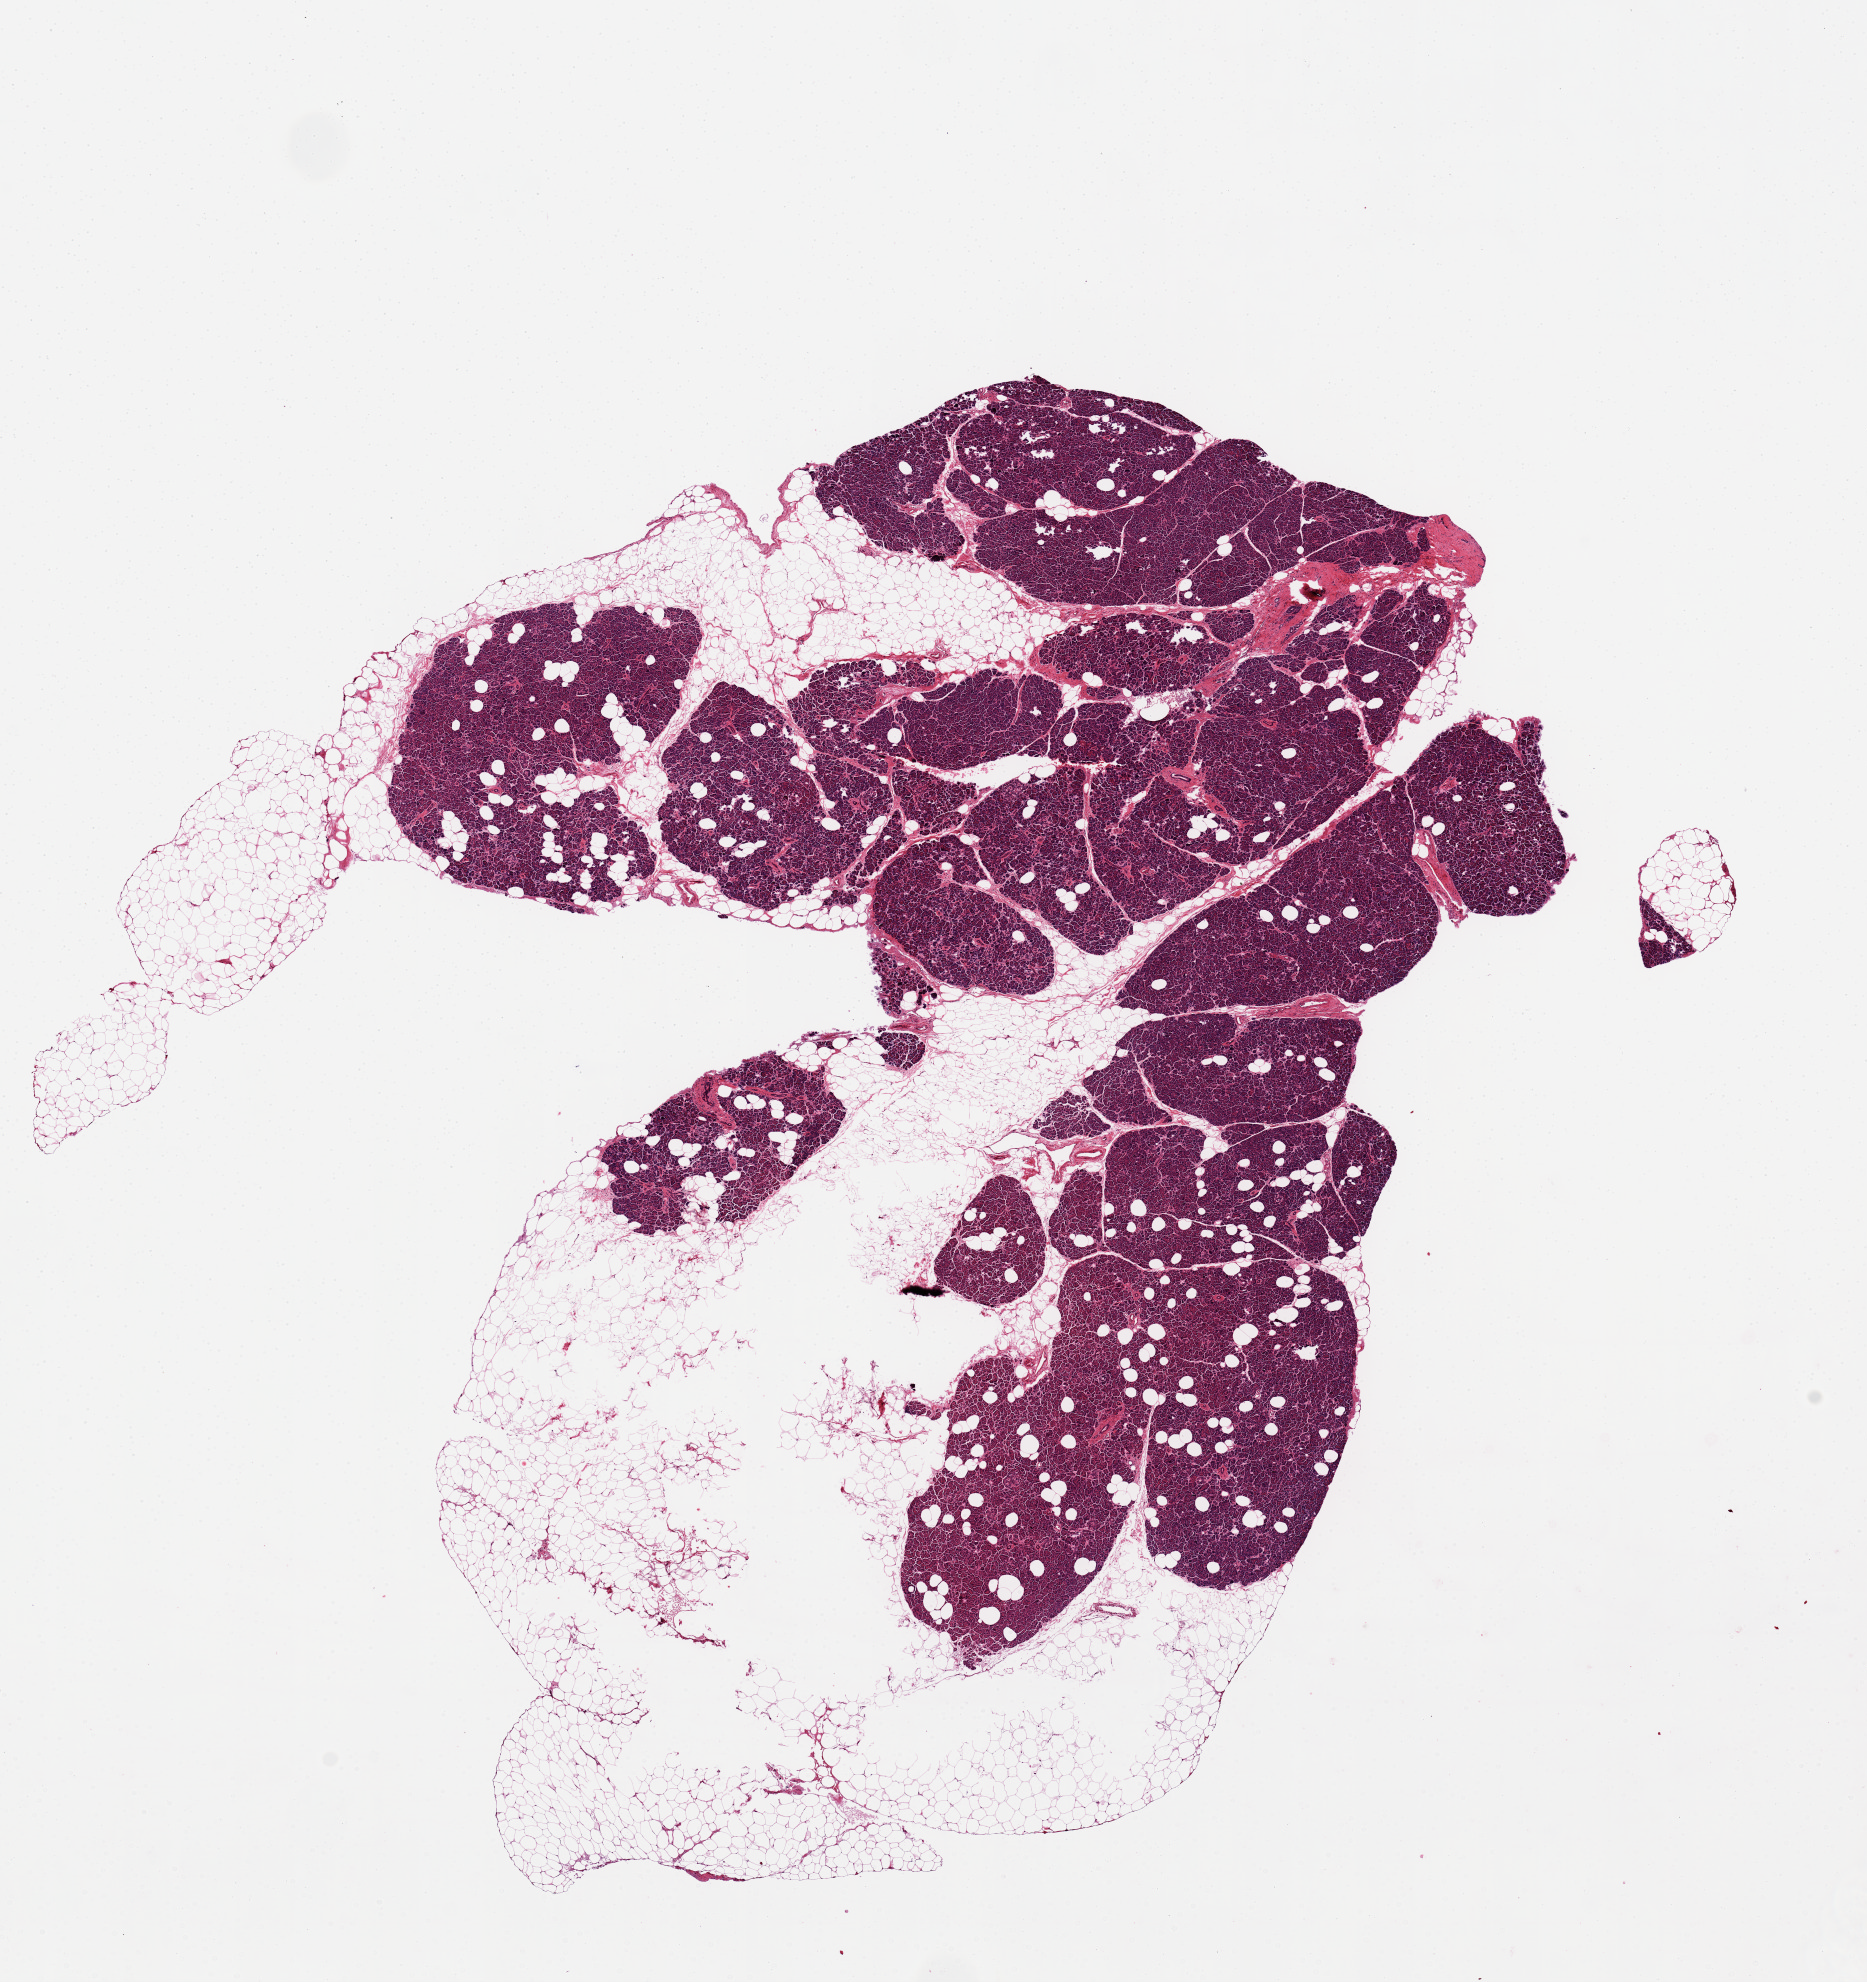
Whole-slide image, hematoxylin and eosin (H&E) stain, shown as a low-resolution overview of the whole scanned area (about 14.8 x 15.7 mm), PAXgene-fixed, paraffin-embedded tissue, sampled site (target tissue): pancreas, tissue donor sample.
Review note (as recorded): 50% fat within and outside parenchyma; 13x10mm.